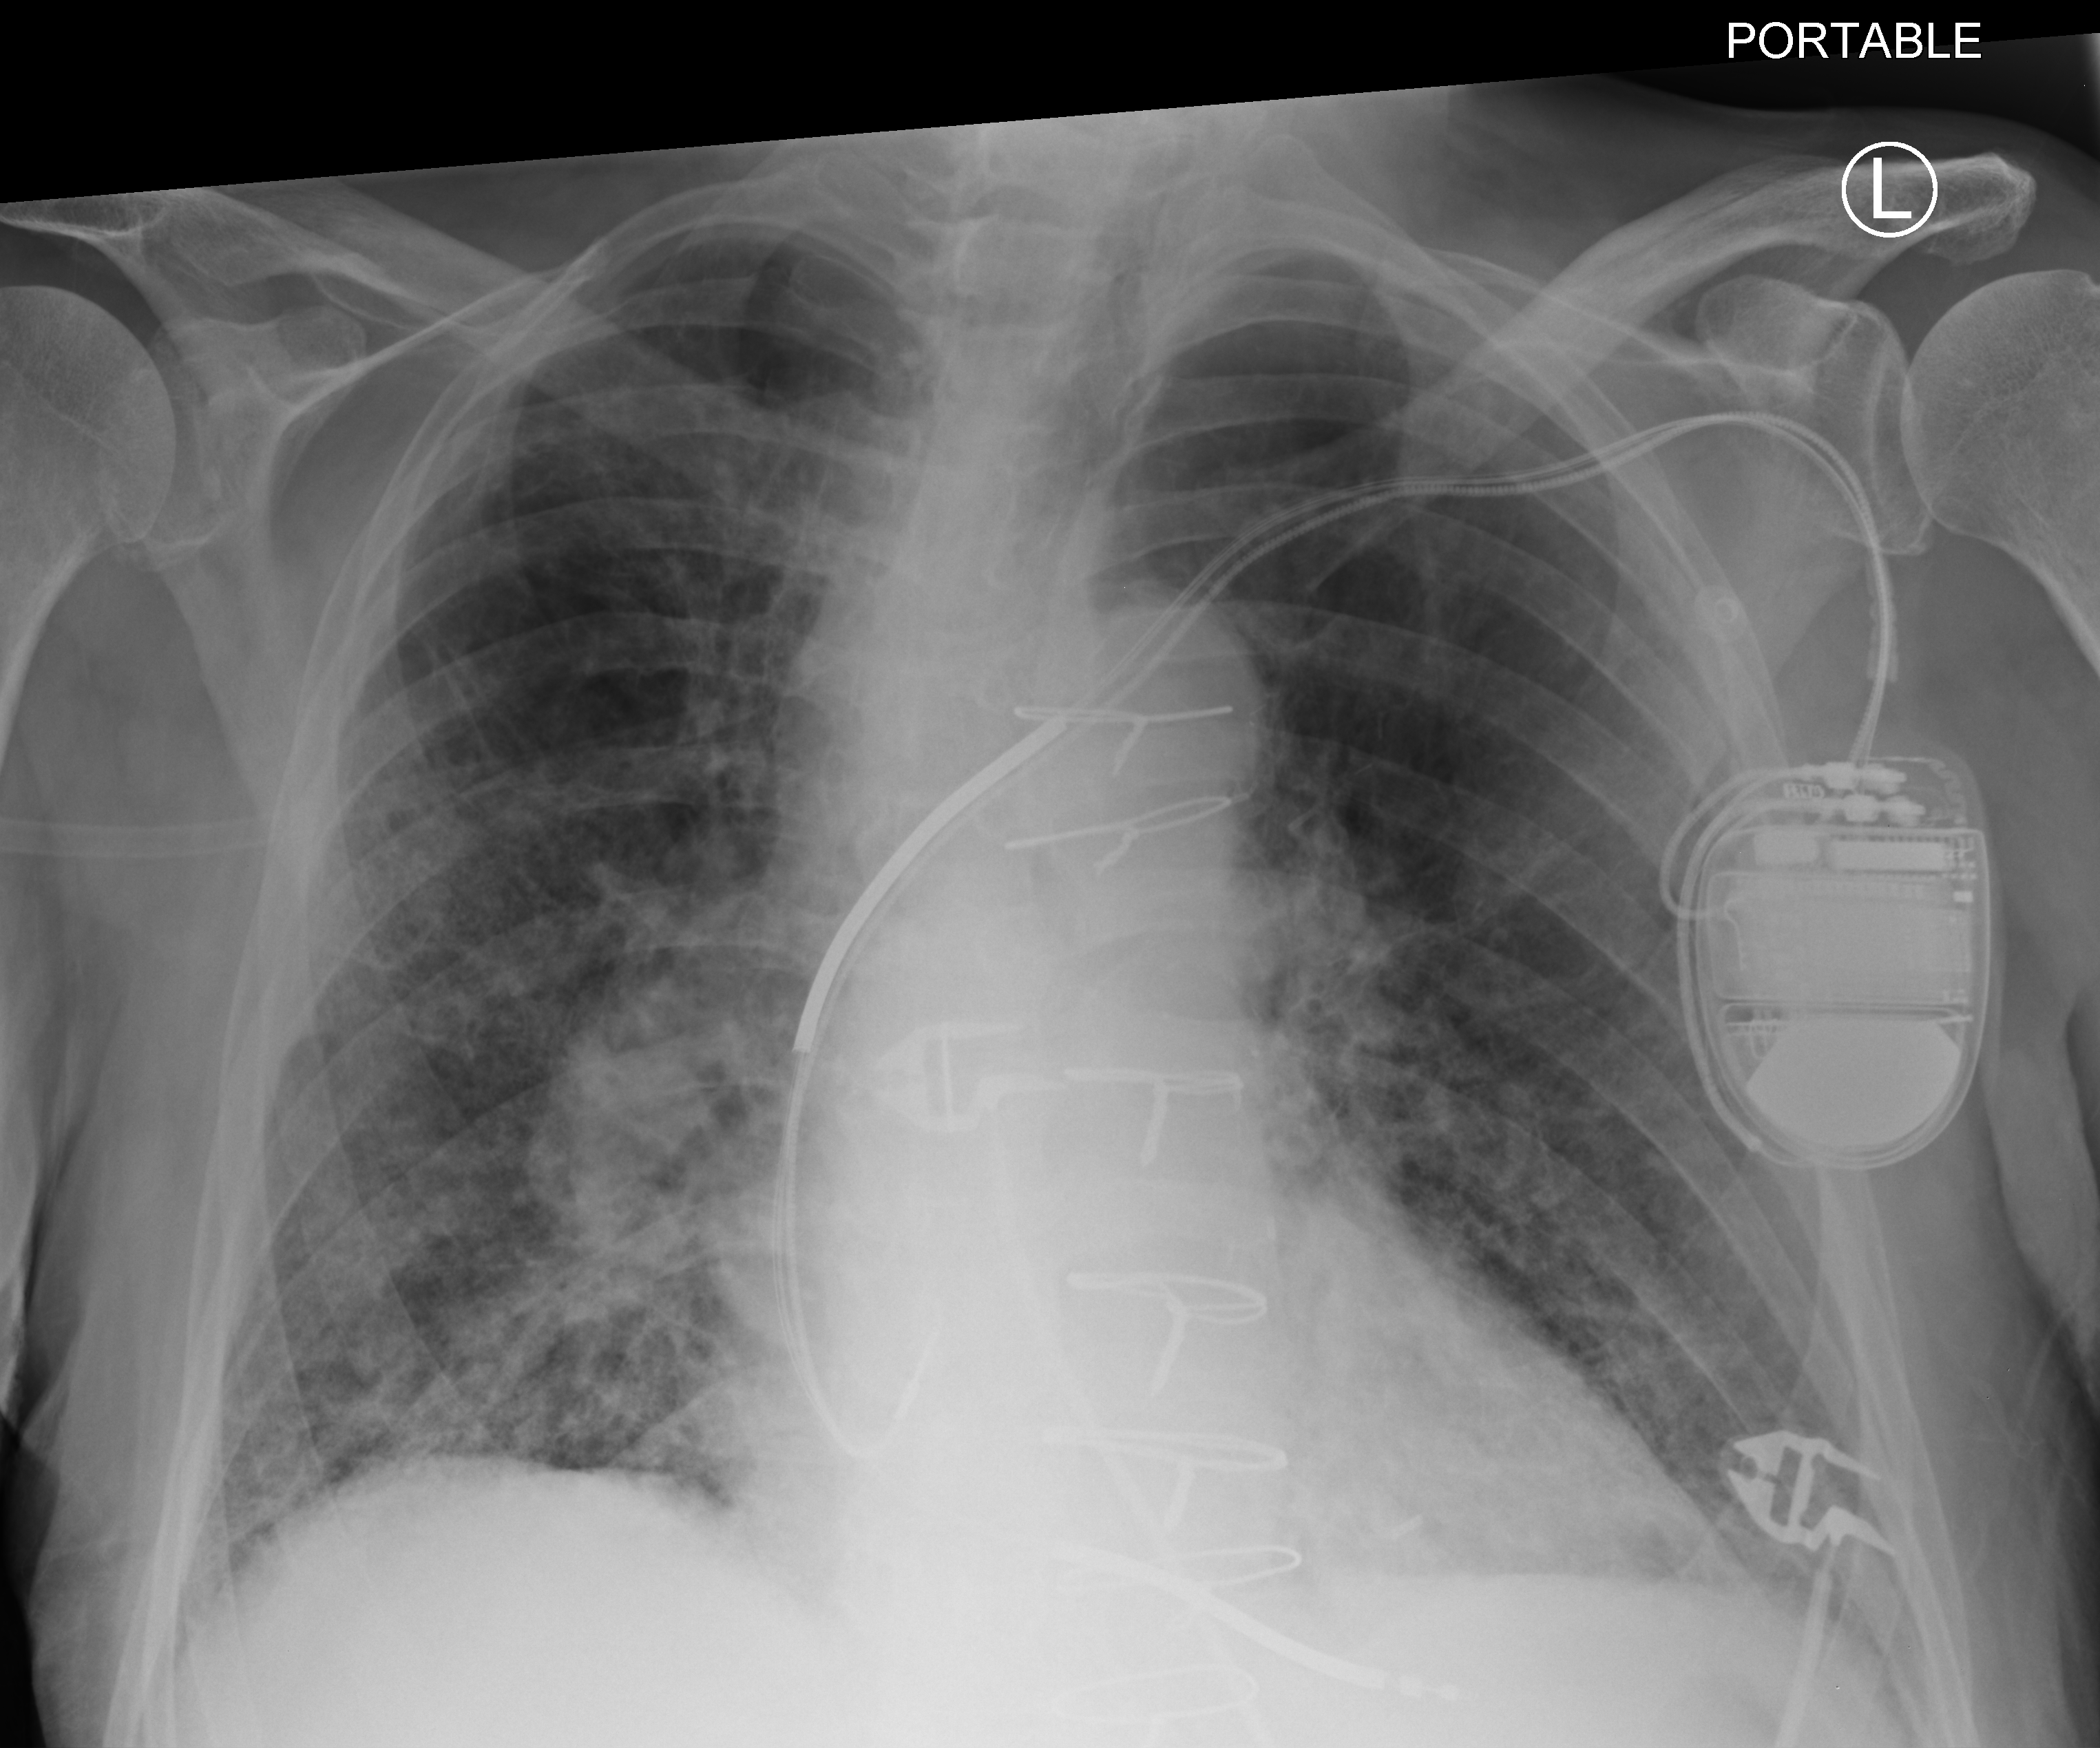
Chest X-ray (portable), anteroposterior (AP) projection. Patient hospitalised with COVID-19; male, aged 75–90 years.
Hospital-stay facts (about this admission, not read from this image; timing relative to this image not recorded): chronic kidney disease (admission record): yes; mechanically ventilated during this hospital stay: no.